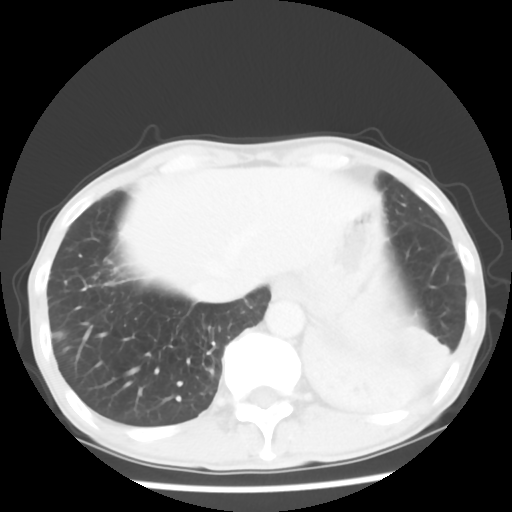
Chest CT, one axial slice; slice 10 of 64 in the series (ordered by position); reconstruction kernel STANDARD; 120 kVp; lung window (W 1500 / L -600 HU); 5 mm slice thickness; 512 × 512 image matrix, field of view 313 × 313 mm. Patient: male, 68 years. From the clinical record (not read from this slice): clinical TNM (as recorded): T4 N0 M0.
Outlined on this slice (bounding box drawn by a radiologist):
- lung tumour (recorded histology: squamous cell carcinoma): box from (x=298, y=307) to (x=459, y=441) px